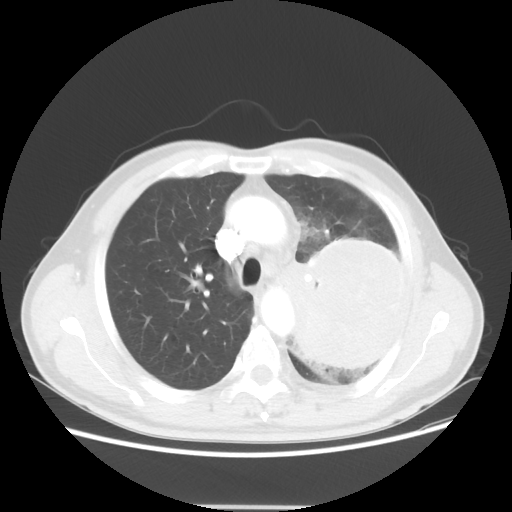
Chest CT, one axial slice. Slice 38 of 53 in the series (ordered by position). Reconstruction kernel STANDARD. 100 kVp. Lung window (W 1500 / L -600 HU). 5 mm slice thickness. 512 × 512 image matrix, field of view 391 × 391 mm. Patient: male, 60 years. Case-level facts recorded for this patient, not image findings: clinical TNM (as recorded): T4 N1 M1a; histopathological grade: G3.
Structures marked on this image (rectangle marked by the reading radiologist):
- lung tumour (recorded histology: large cell carcinoma): box from (x=286, y=236) to (x=407, y=387) px